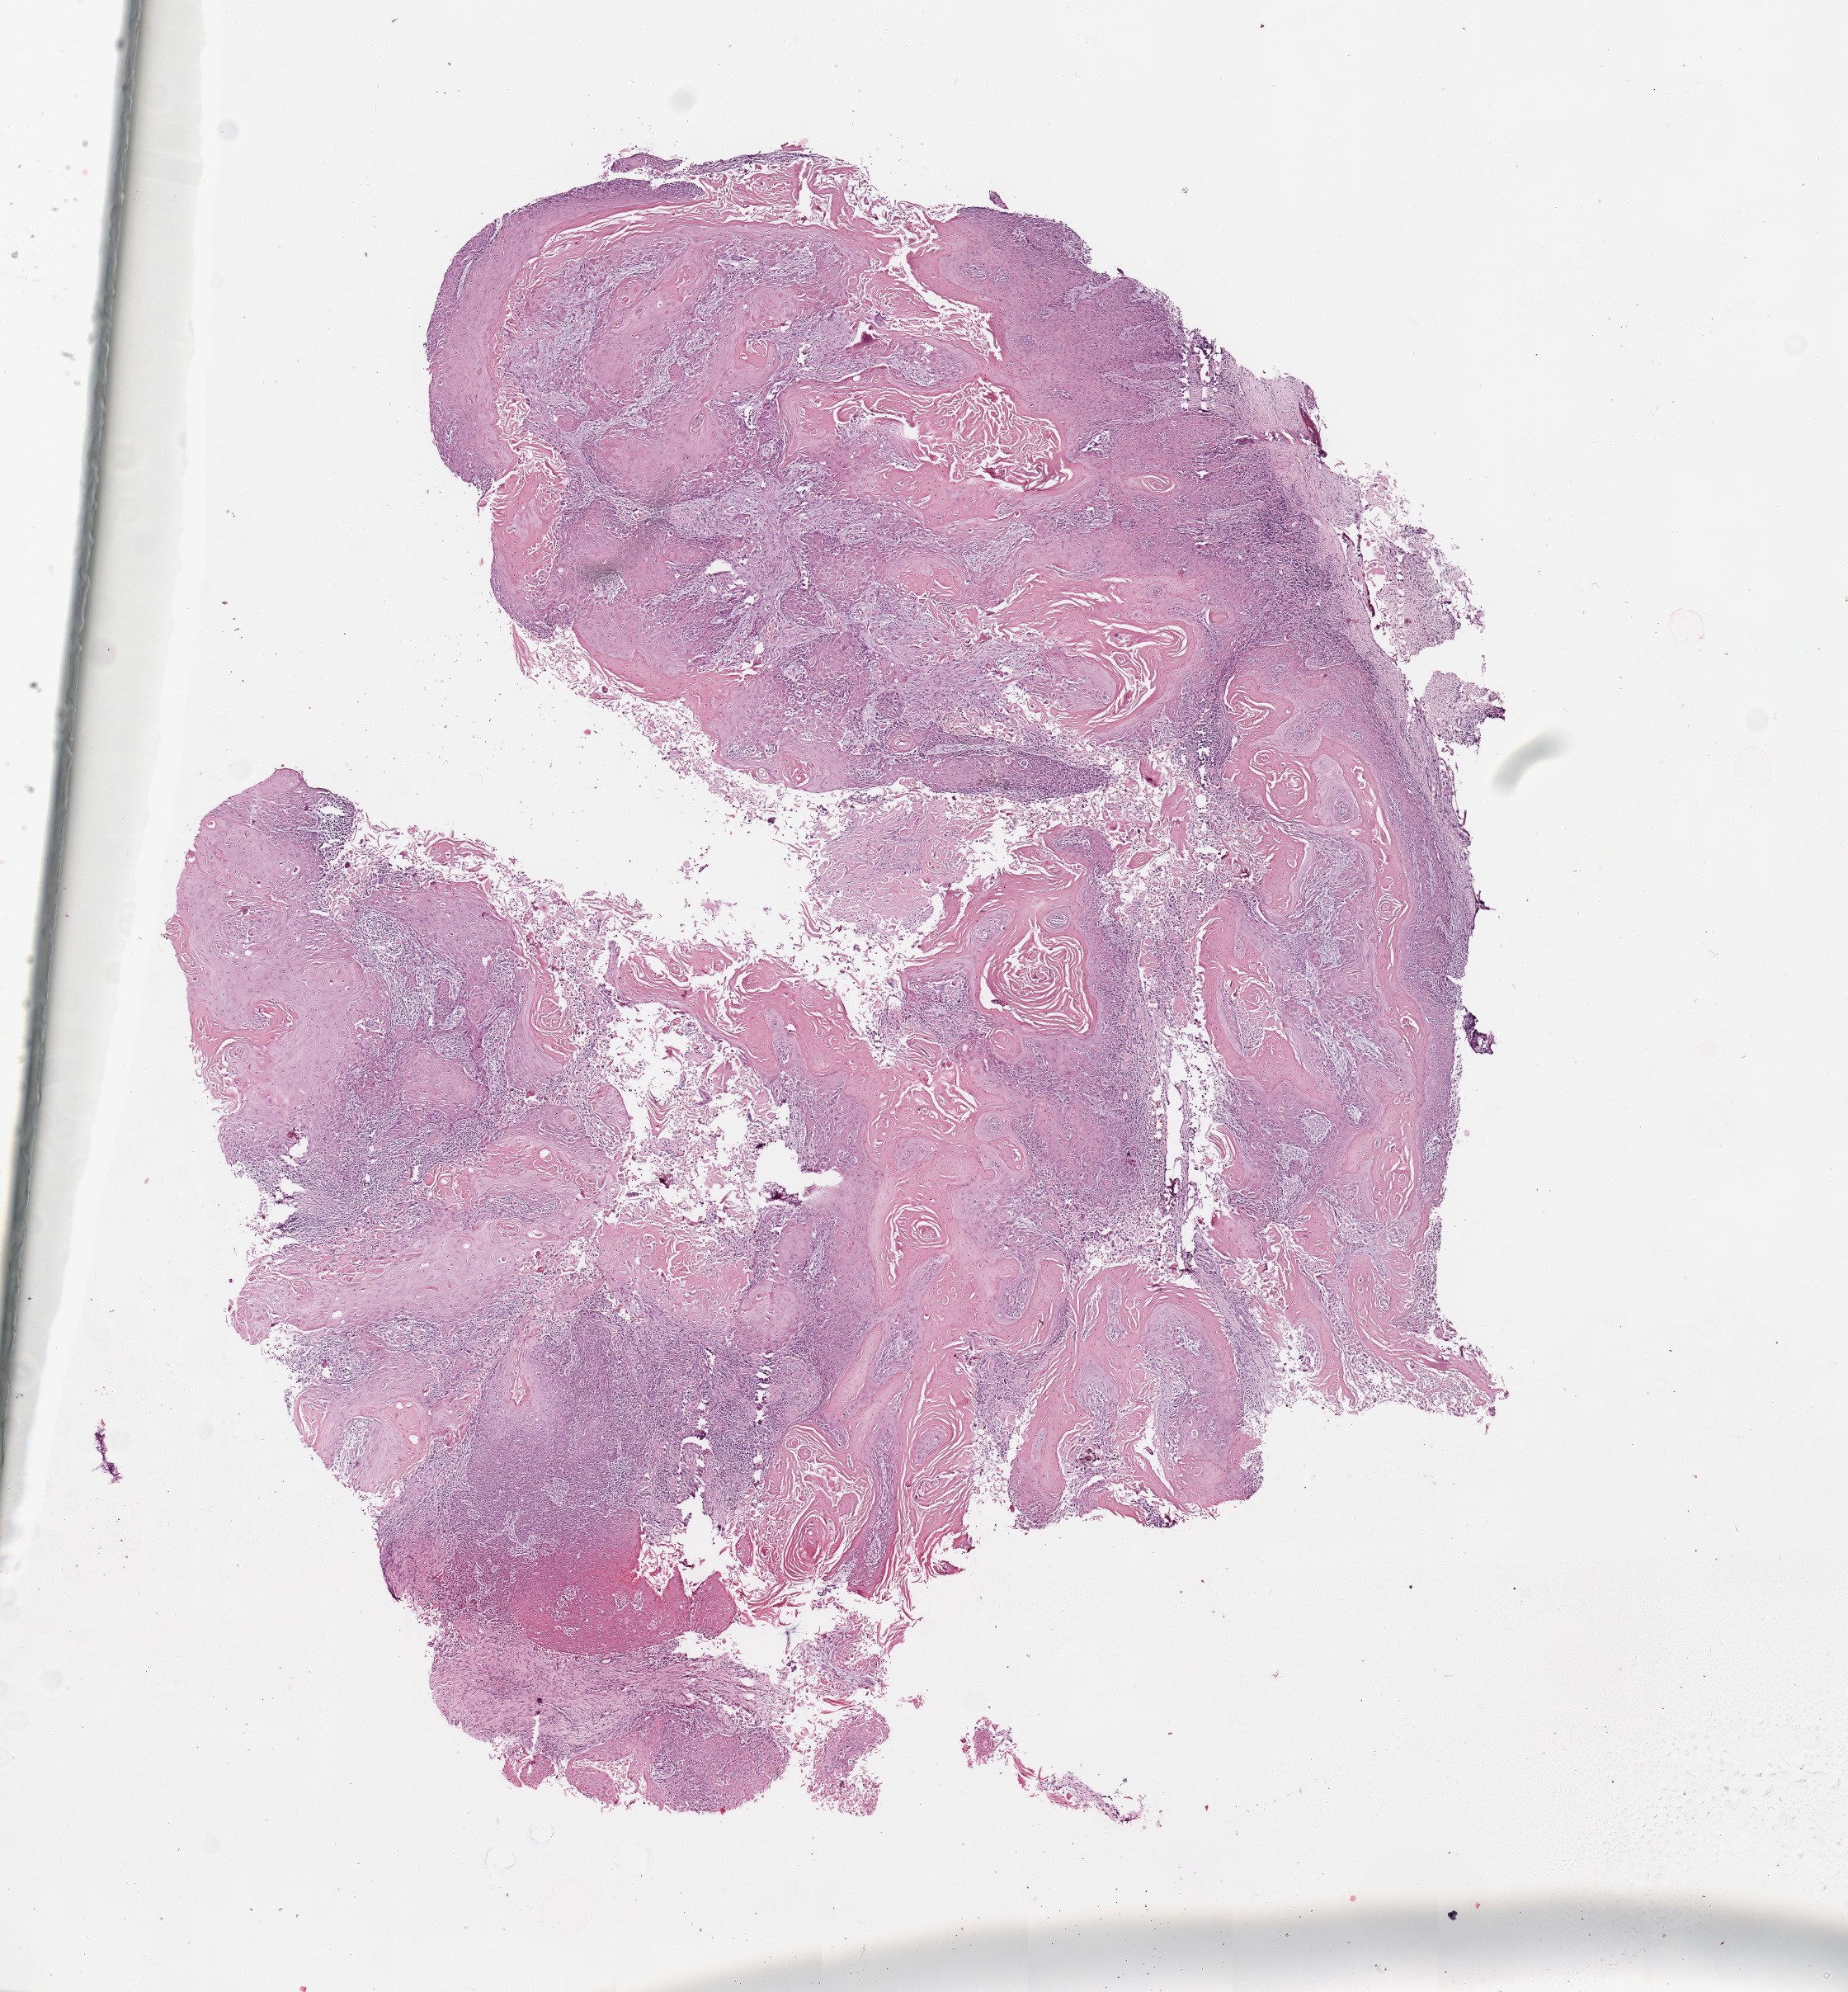
Digitized H&E tissue section (whole slide), shown as a low-resolution overview of the whole scanned area (about 8.9 x 9.5 mm, slide scanned at 20x); head and neck, tissue type not recorded. Patient: female, age 53 years.
Patient diagnosis: Squamous cell carcinoma, NOS (gum, NOS).